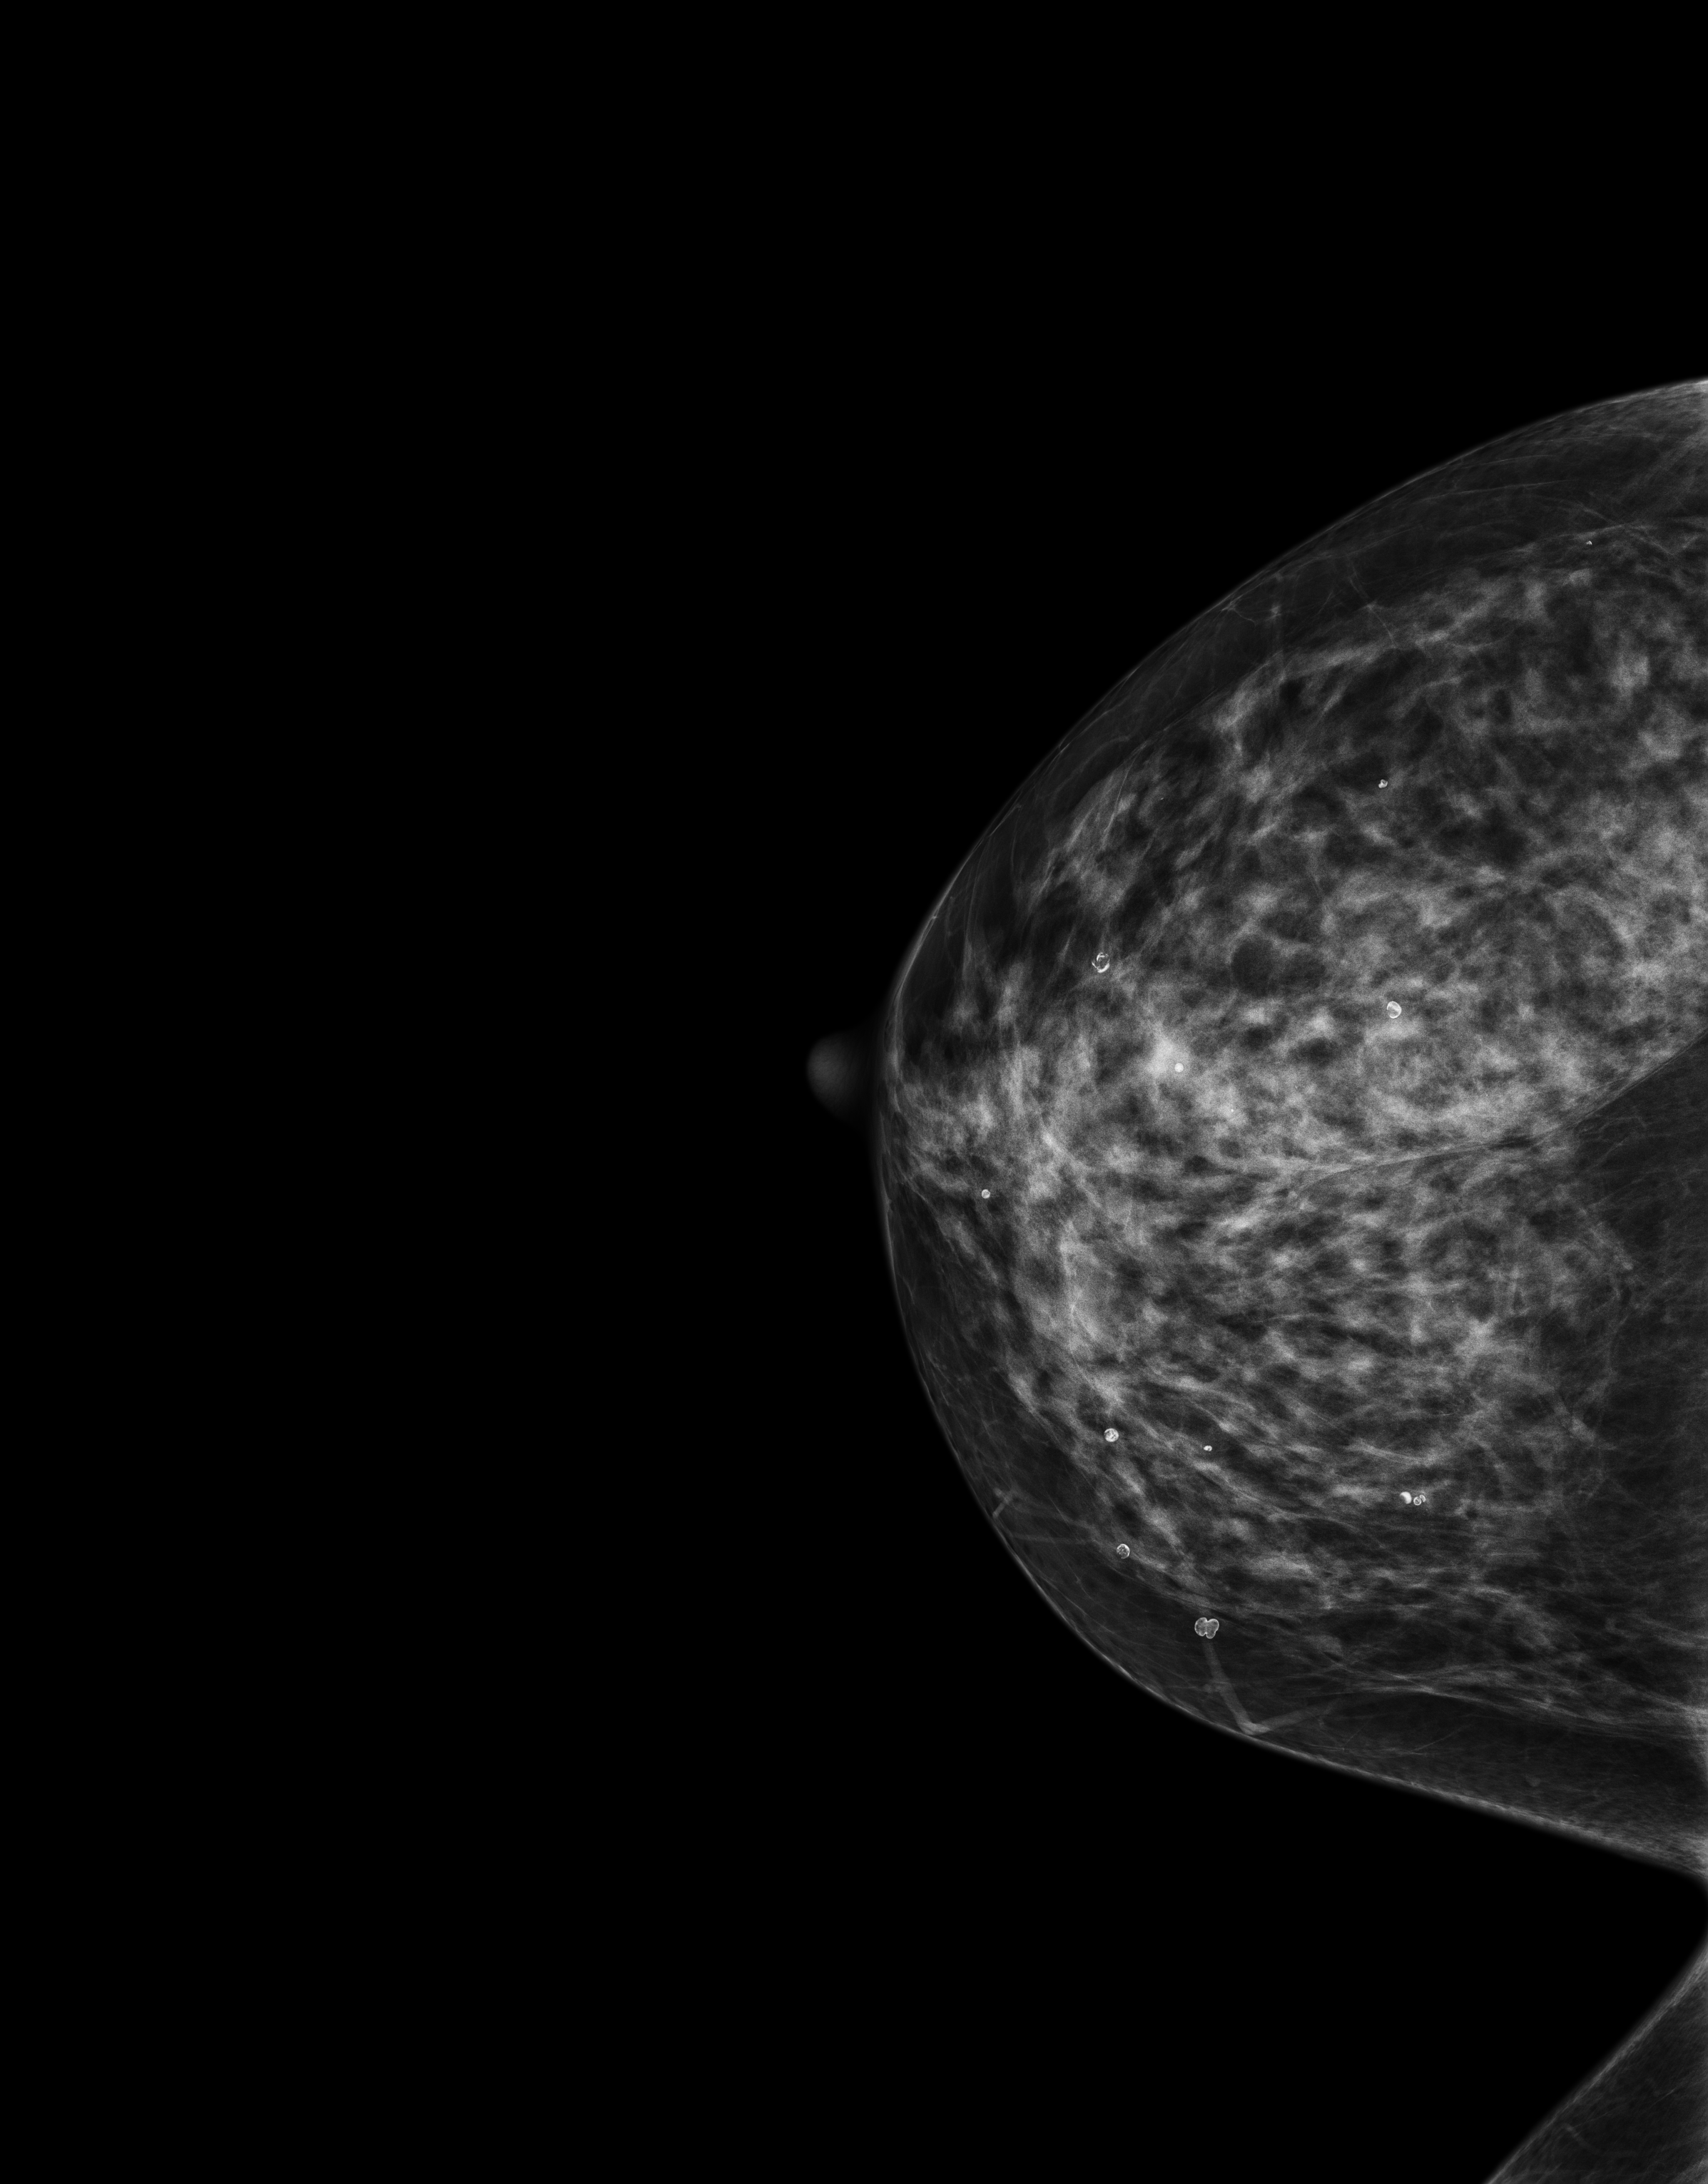
Digital mammogram (FFDM), right breast, CC view, screening examination, compressed breast thickness 58 mm, system: Senographe Essential ADS_56.21.3. Patient: female, 66 years.
- breast density at the screening exam (both breasts): heterogeneously dense (BI-RADS density category c)
- final BI-RADS category for the screening round (tomosynthesis exam, both breasts): category 1
- recall: no recall after this screen